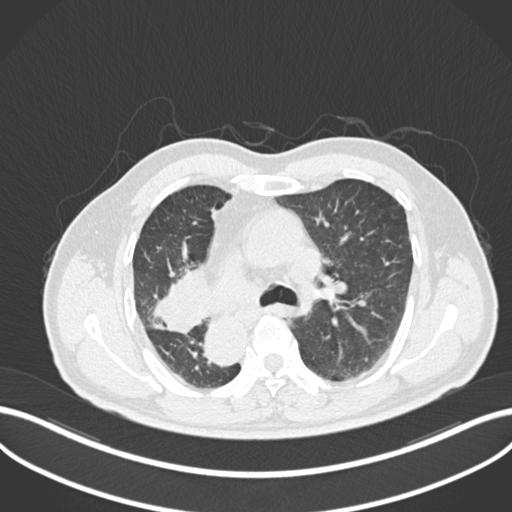
Chest CT, one axial slice. Slice 153 of 206 in the series (ordered by position). Reconstruction kernel B30f. Lung window (W 1500 / L -600 HU). 512 × 512 image matrix, field of view 400 × 400 mm. Patient: male, 67 years. Case-level facts recorded for this patient, not image findings: clinical TNM (as recorded): T2a N0 M0.
Annotated regions visible in this slice (bounding box drawn by a radiologist):
- lung tumour (recorded histology: squamous cell carcinoma): bounding box <150,259,214,335> (left, top, right, bottom; pixels)